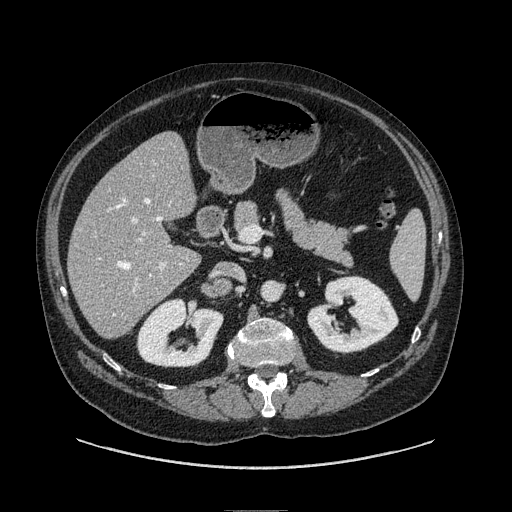
Contrast-enhanced abdominal CT, one axial slice; position 32 of 149 along the scan axis; soft-tissue window (W 400 / L 40 HU); 1.25 mm slice thickness; 512 × 512 image matrix, field of view 440 × 440 mm. Male patient. From the clinical record (not read from this slice): diagnosis: adrenocortical carcinoma; tumour side: right adrenal; tumour size at pathology: 7.5 cm; Ki-67 index: 15 %; stage (as recorded): 2.
Annotated regions visible in this slice (semi-automatic segmentation, software-assisted and operator-edited):
- mass: bounding box [x1, y1, x2, y2] px = [203, 282, 230, 299]